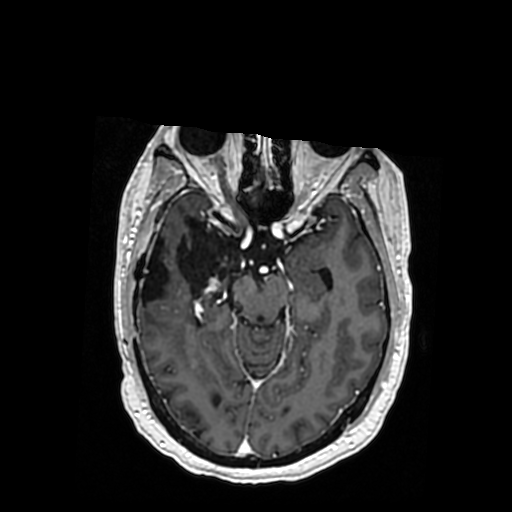
Brain MRI from a brain-tumour surgery series, one axial slice. Position 216 of 364 along the scan axis. T1-weighted post-contrast. 0.5 mm slice thickness. 512 × 512 image matrix, field of view 260 × 260 mm. From the clinical record (not read from this slice): histopathology: Oligodendroglioma; WHO grade: 3; IDH mutation: yes.
Annotated regions visible in this slice (expert manual segmentation):
- previous resection cavity: box from (x=140, y=220) to (x=240, y=303) px